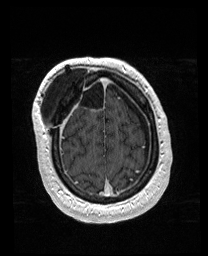
Brain MRI from a brain-tumour surgery series, one axial slice. Slice 40 of 176 in the series (ordered by position). T1-weighted post-contrast. 1 mm slice thickness. 208 × 256 image matrix. Case-level facts recorded for this patient, not image findings: histopathology: Astrocytoma; WHO grade: 4; IDH mutation: yes; tumour location: Right Orbitofrontal Anterior Temporal Insular.
Structures marked on this image (outlined manually by an expert reader):
- previous resection cavity: bounding box <63,79,87,107> (left, top, right, bottom; pixels)